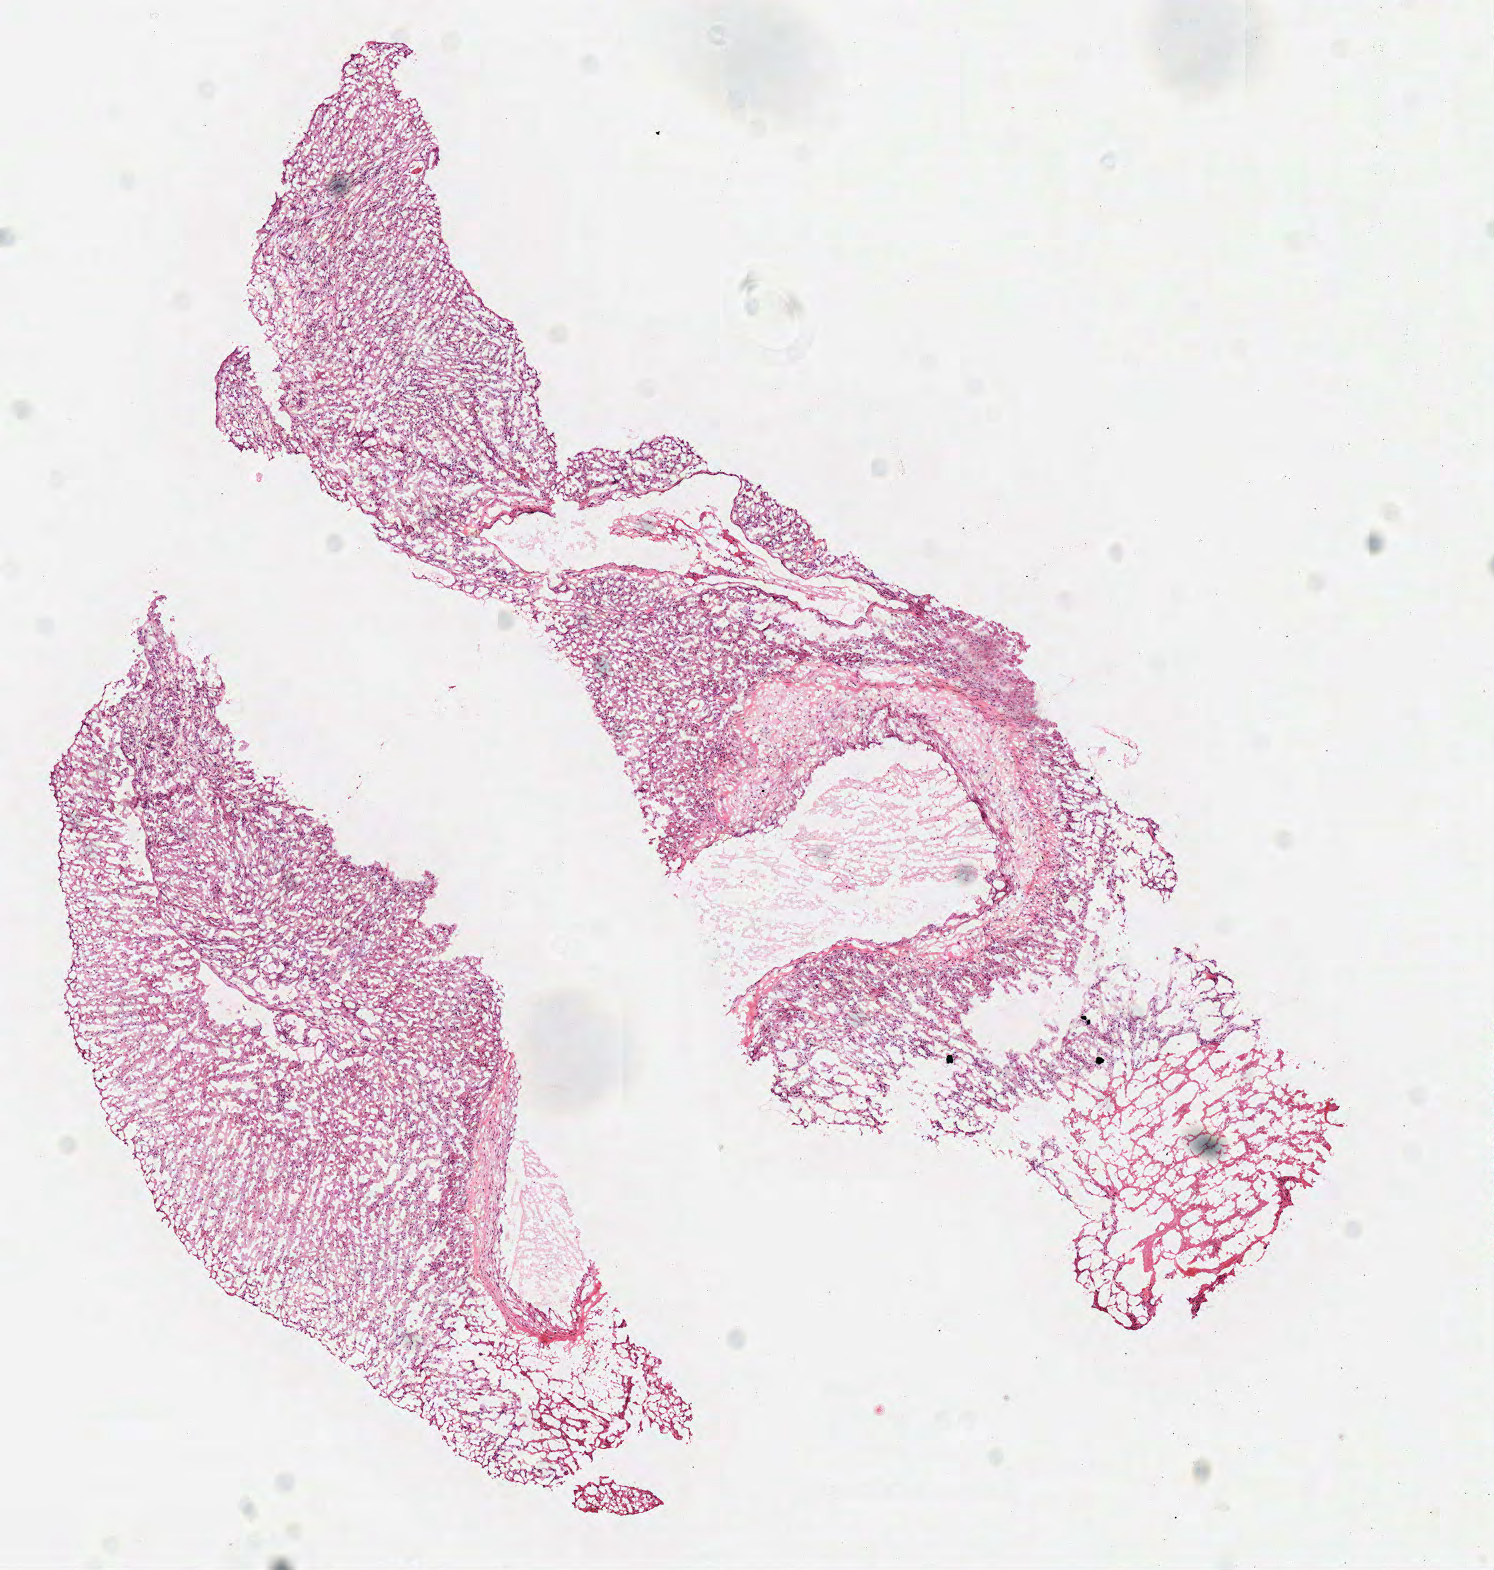
Whole-slide histology image, Hematoxylin and eosin (H&E) stained — a low-resolution overview of the entire scanned area, about 5.9 x 6.2 mm (acquisition: 40x scan), frozen section from the top of the tissue portion, primary tumour sample from the brain. Male, age 62 years at initial diagnosis. Pathologist review of this section (percent, as recorded): tumour cells 90%, tumour nuclei 75%, normal cells 0%, stromal cells 10%, necrosis 10%.
Histologic diagnosis: Glioblastoma.